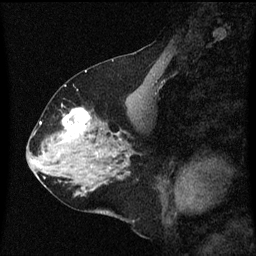
Breast MRI (dynamic contrast-enhanced), one sagittal slice. Slice 27 of 60 in the series (ordered by position). Dynamic contrast-enhanced series, image 2 of 3 at this slice position (ordered by acquisition). 1.5 T. TE 4.2 ms, TR 8 ms. 2 mm slice thickness. 256 × 256 image matrix. Patient: female, 58 years.
Structures marked on this image (semi-automatic segmentation, software-assisted and operator-edited):
- analysis volume of interest (the breast-tissue region the enhancement analysis was run in; not a lesion): bounding box <56,108,99,149> (left, top, right, bottom; pixels)
- tumour enhancement mask (voxels above the 70 % enhancement threshold inside the analysis volume of interest): <63,108,92,143>